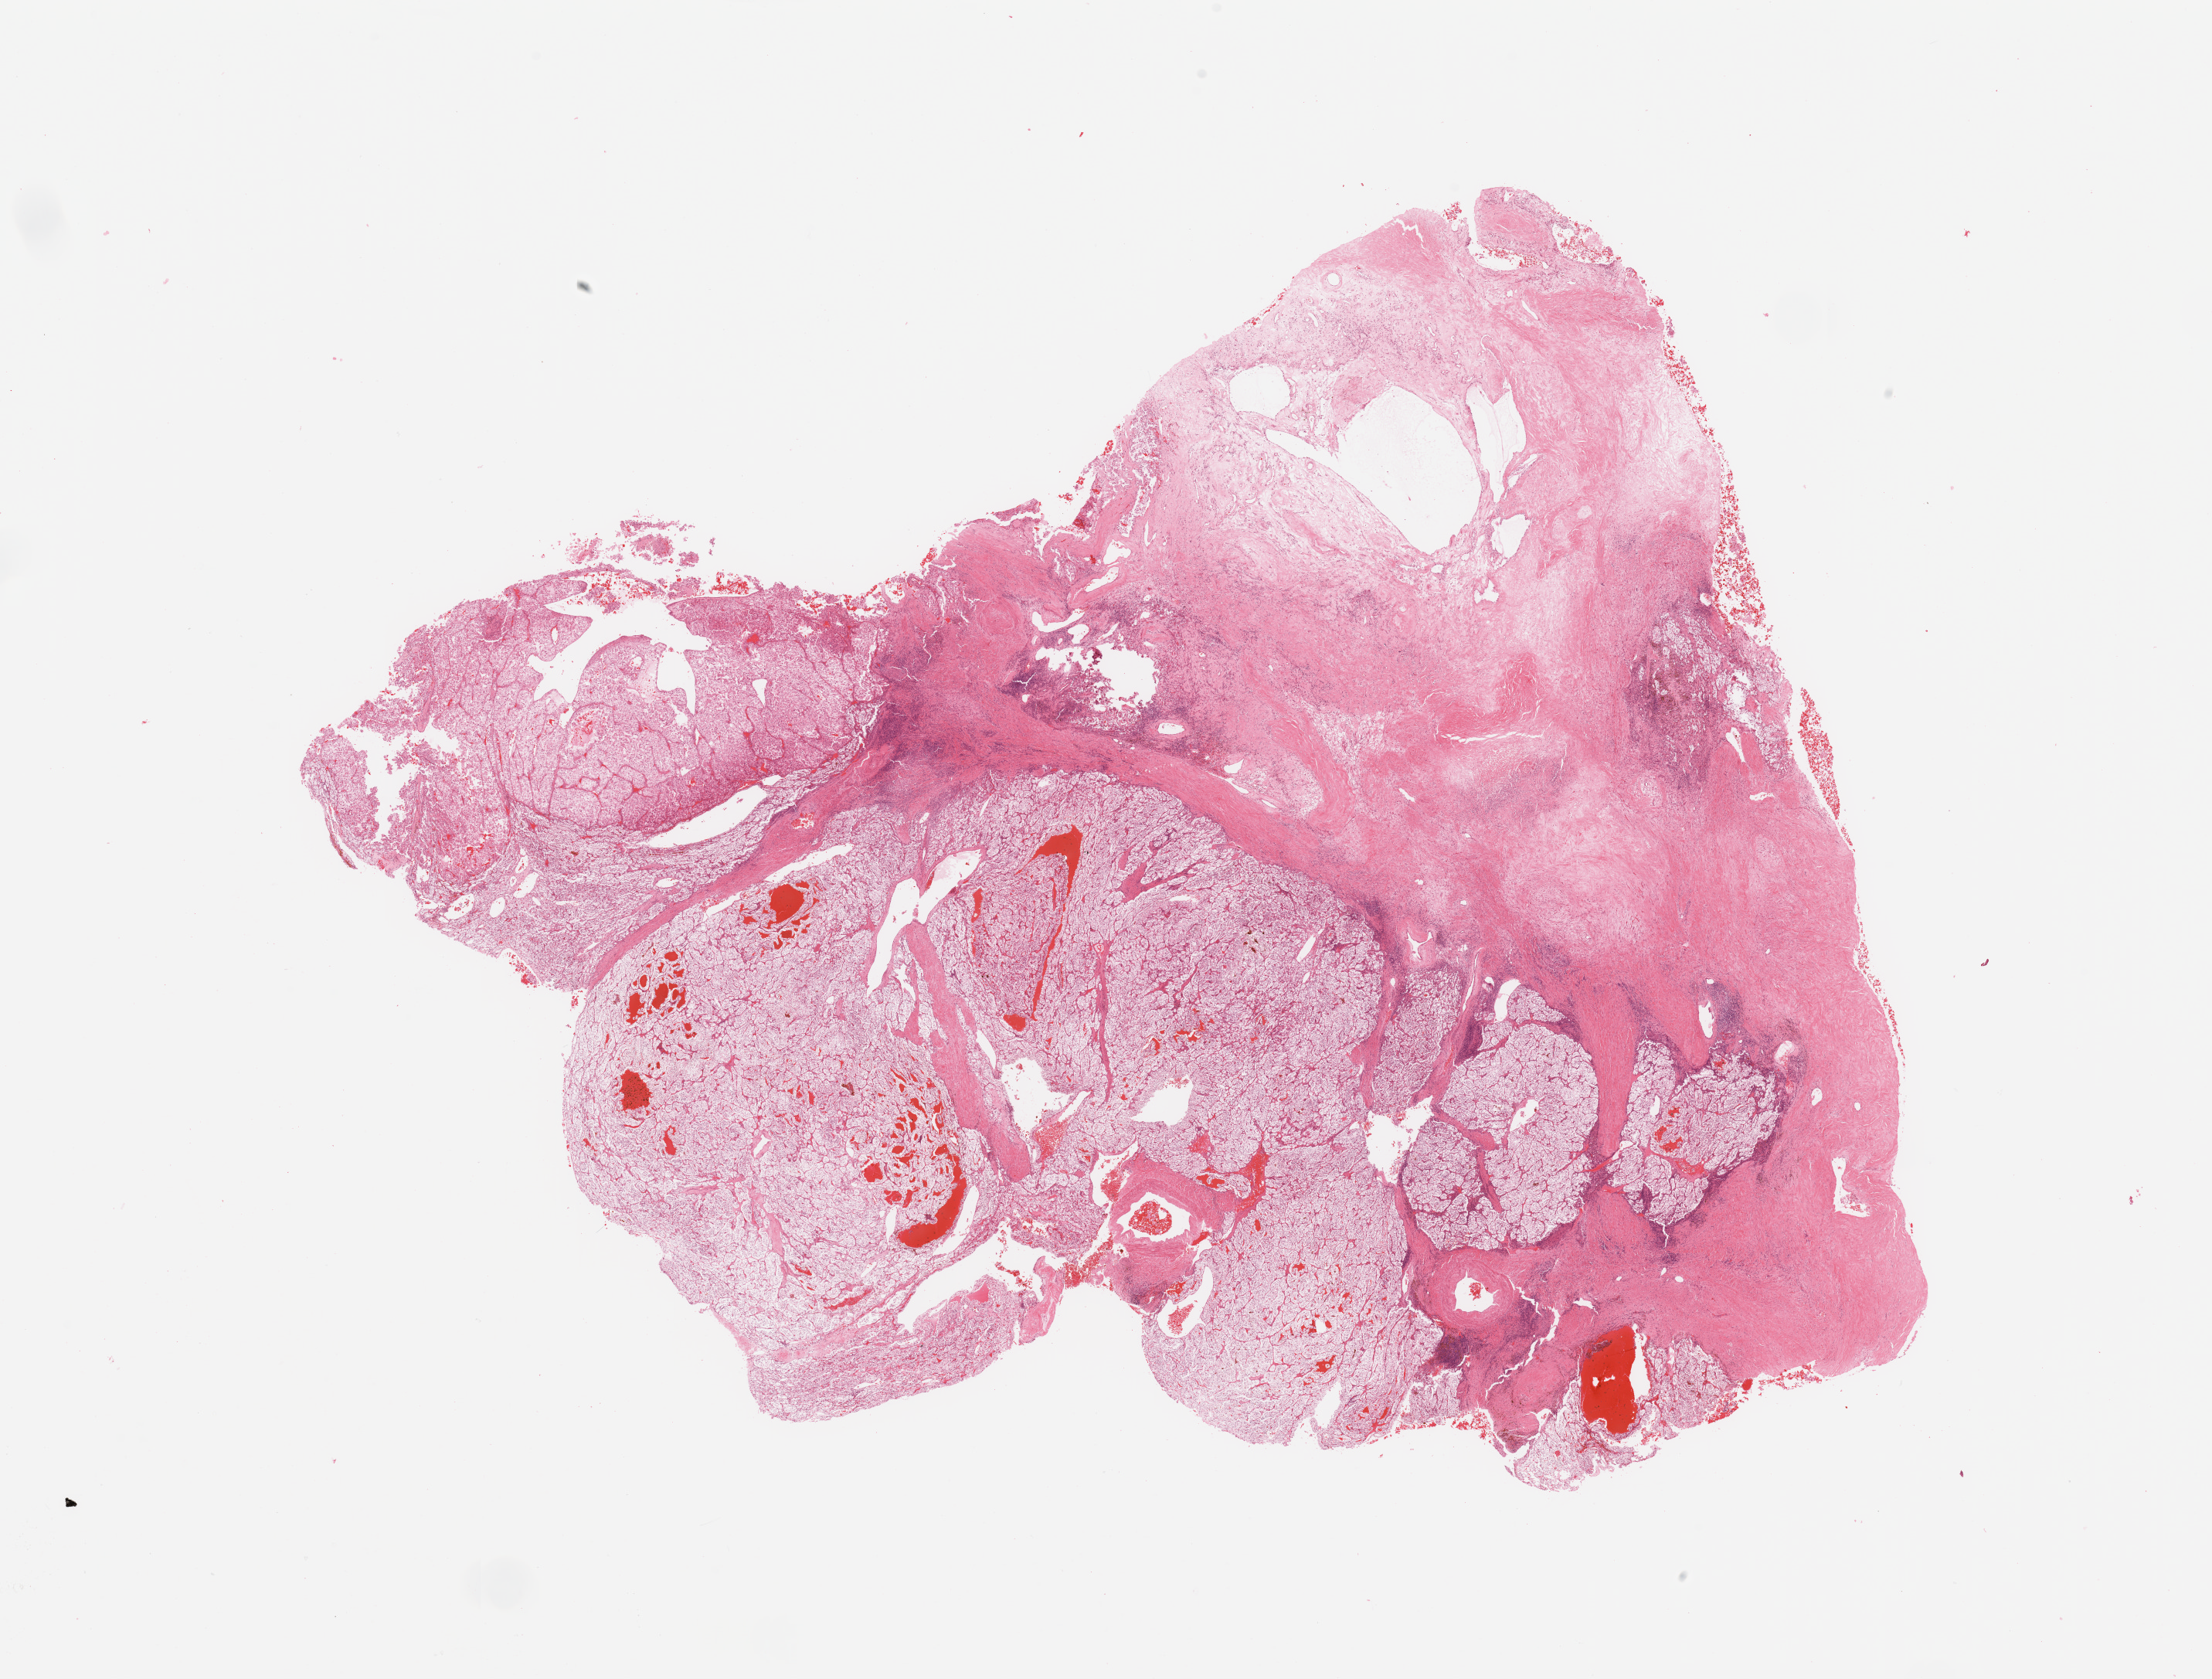
Whole-slide histology image, Hematoxylin and eosin (H&E) stained — low-resolution overview of the scanned area, about 22.6 x 17.2 mm, kidney, tumour tissue. 66-year-old male patient. Histologic grade: G1 (well differentiated).
- histologic diagnosis: Renal cell carcinoma, NOS